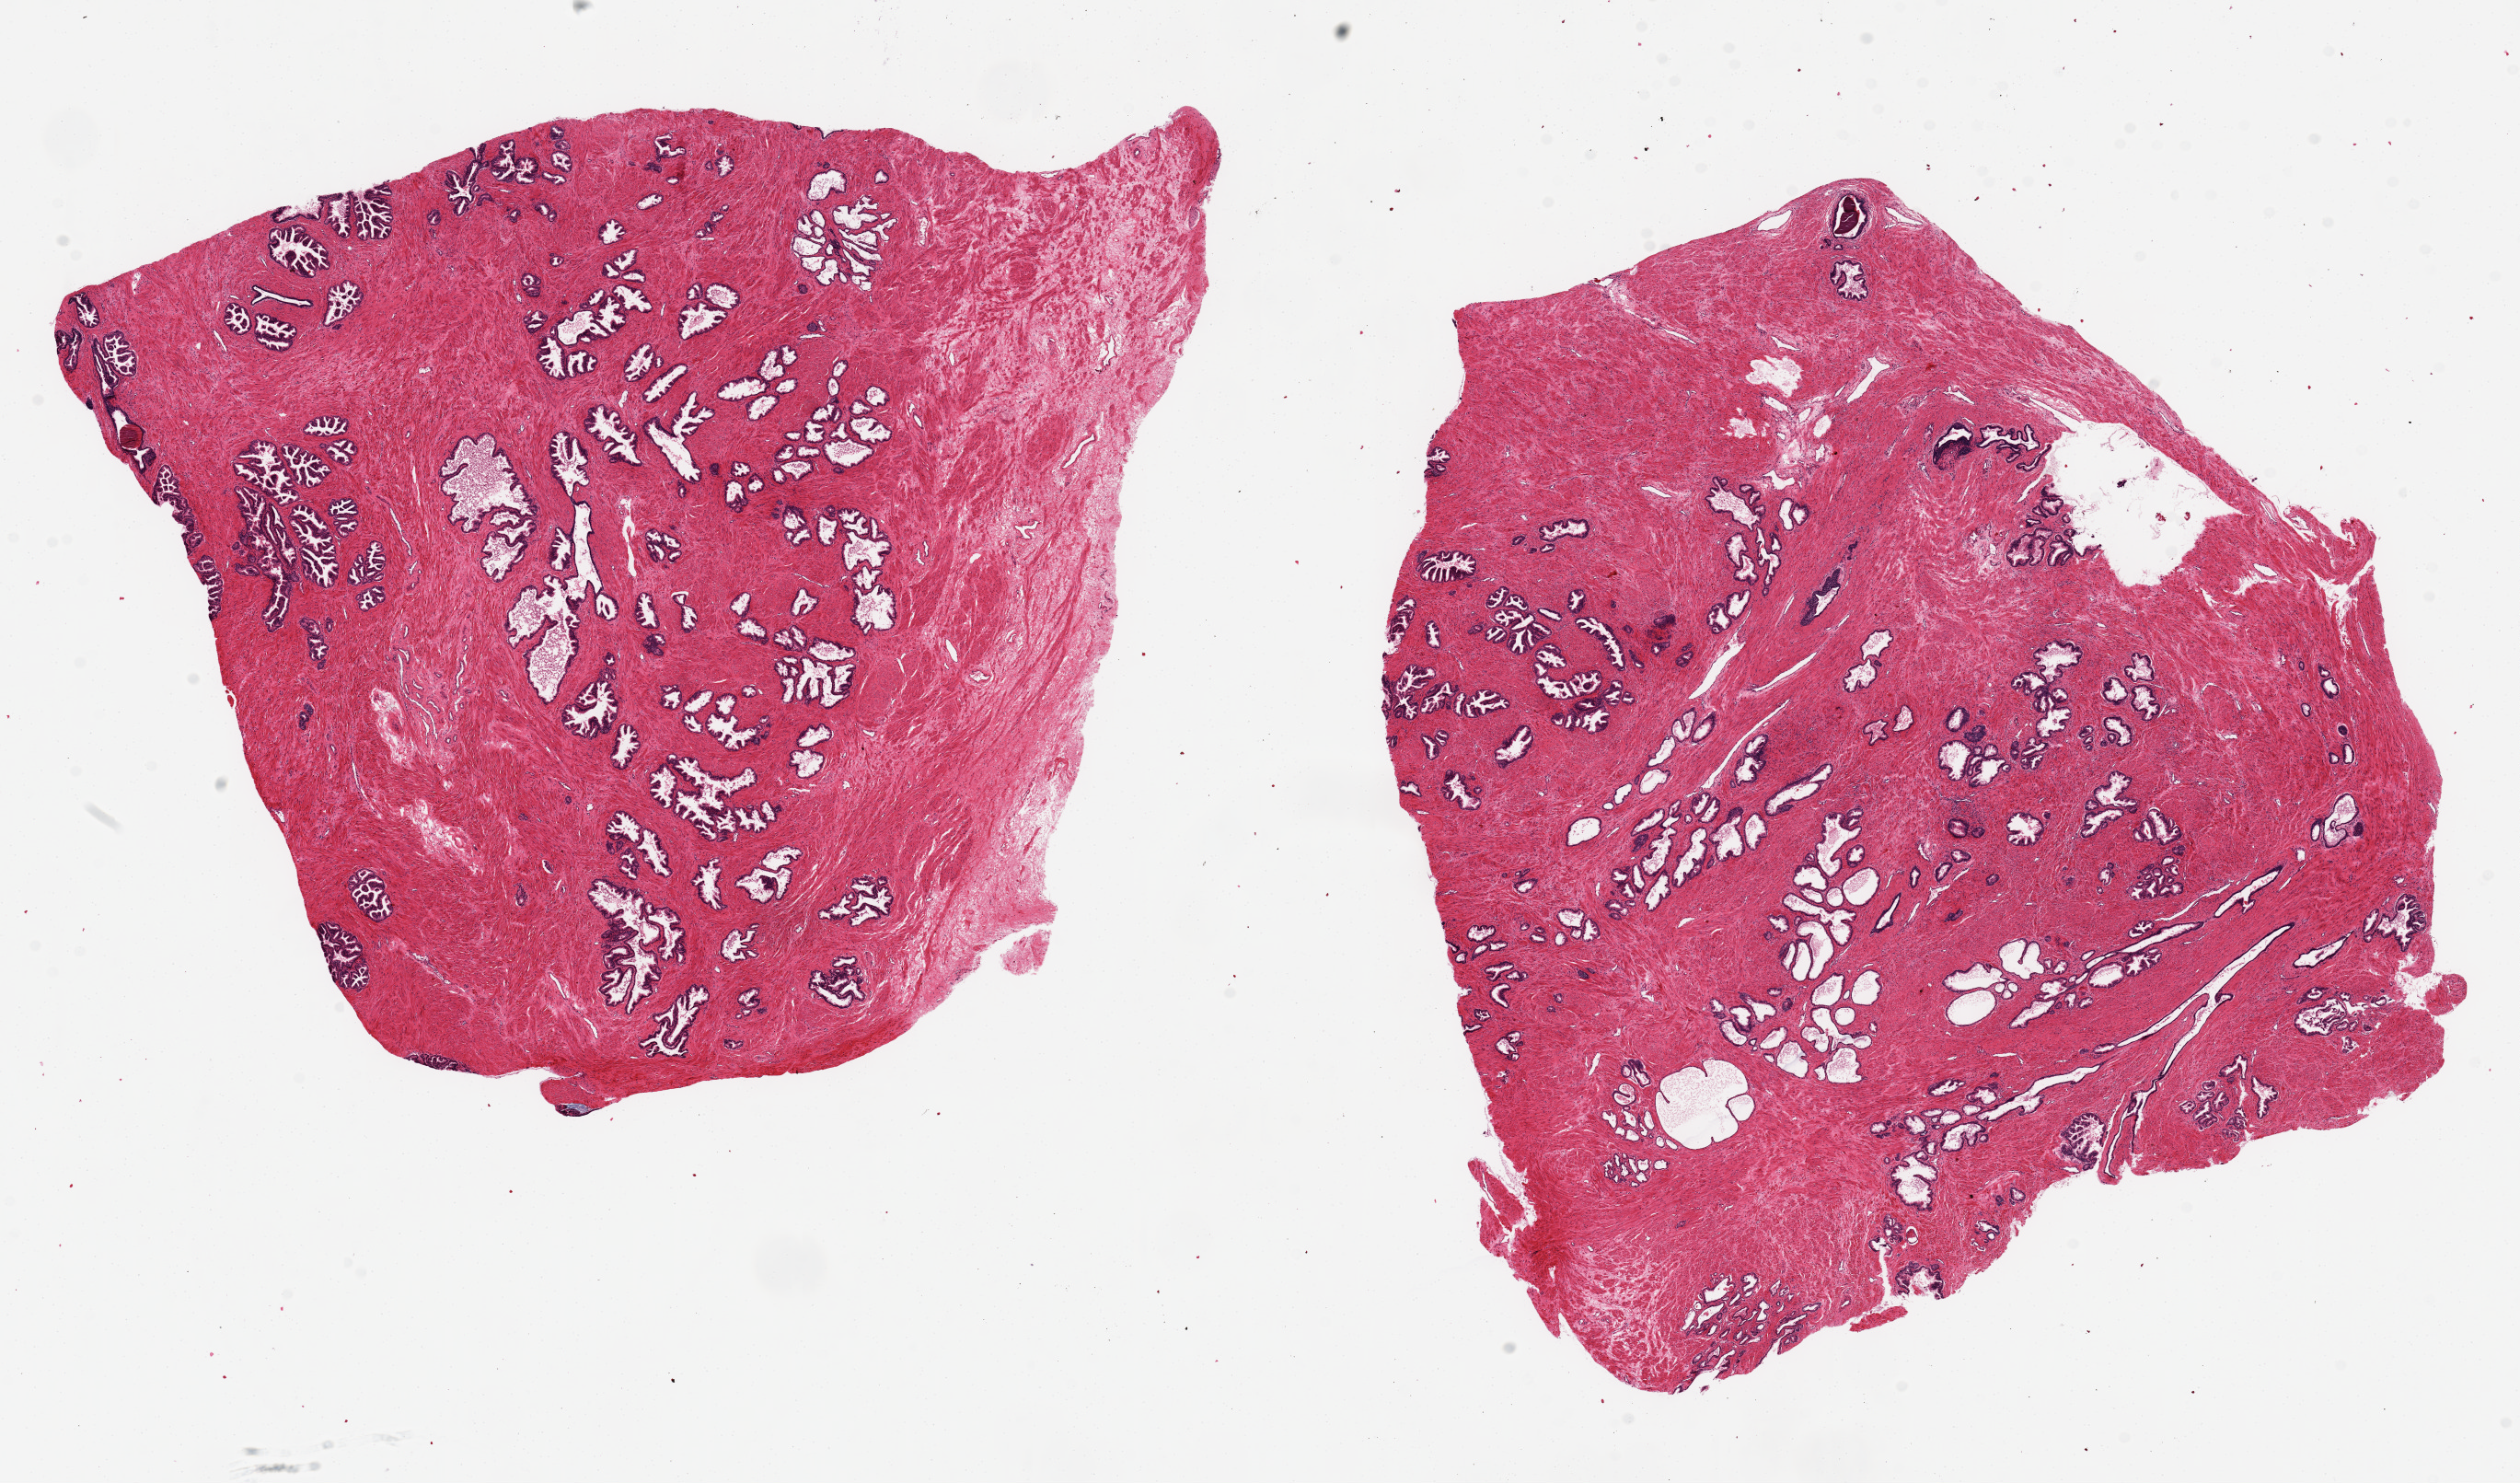
Digitized haematoxylin and eosin-stained section — low-resolution overview of the scanned area, about 21.7 x 12.7 mm. PAXgene-fixed paraffin-embedded (PFPE) section. Section of prostate (target tissue). Tissue donor sample. Donor sex: male.
- pathologist's review note for this sample: 2 pieces ~9x9mm each; no significant hyperplasia